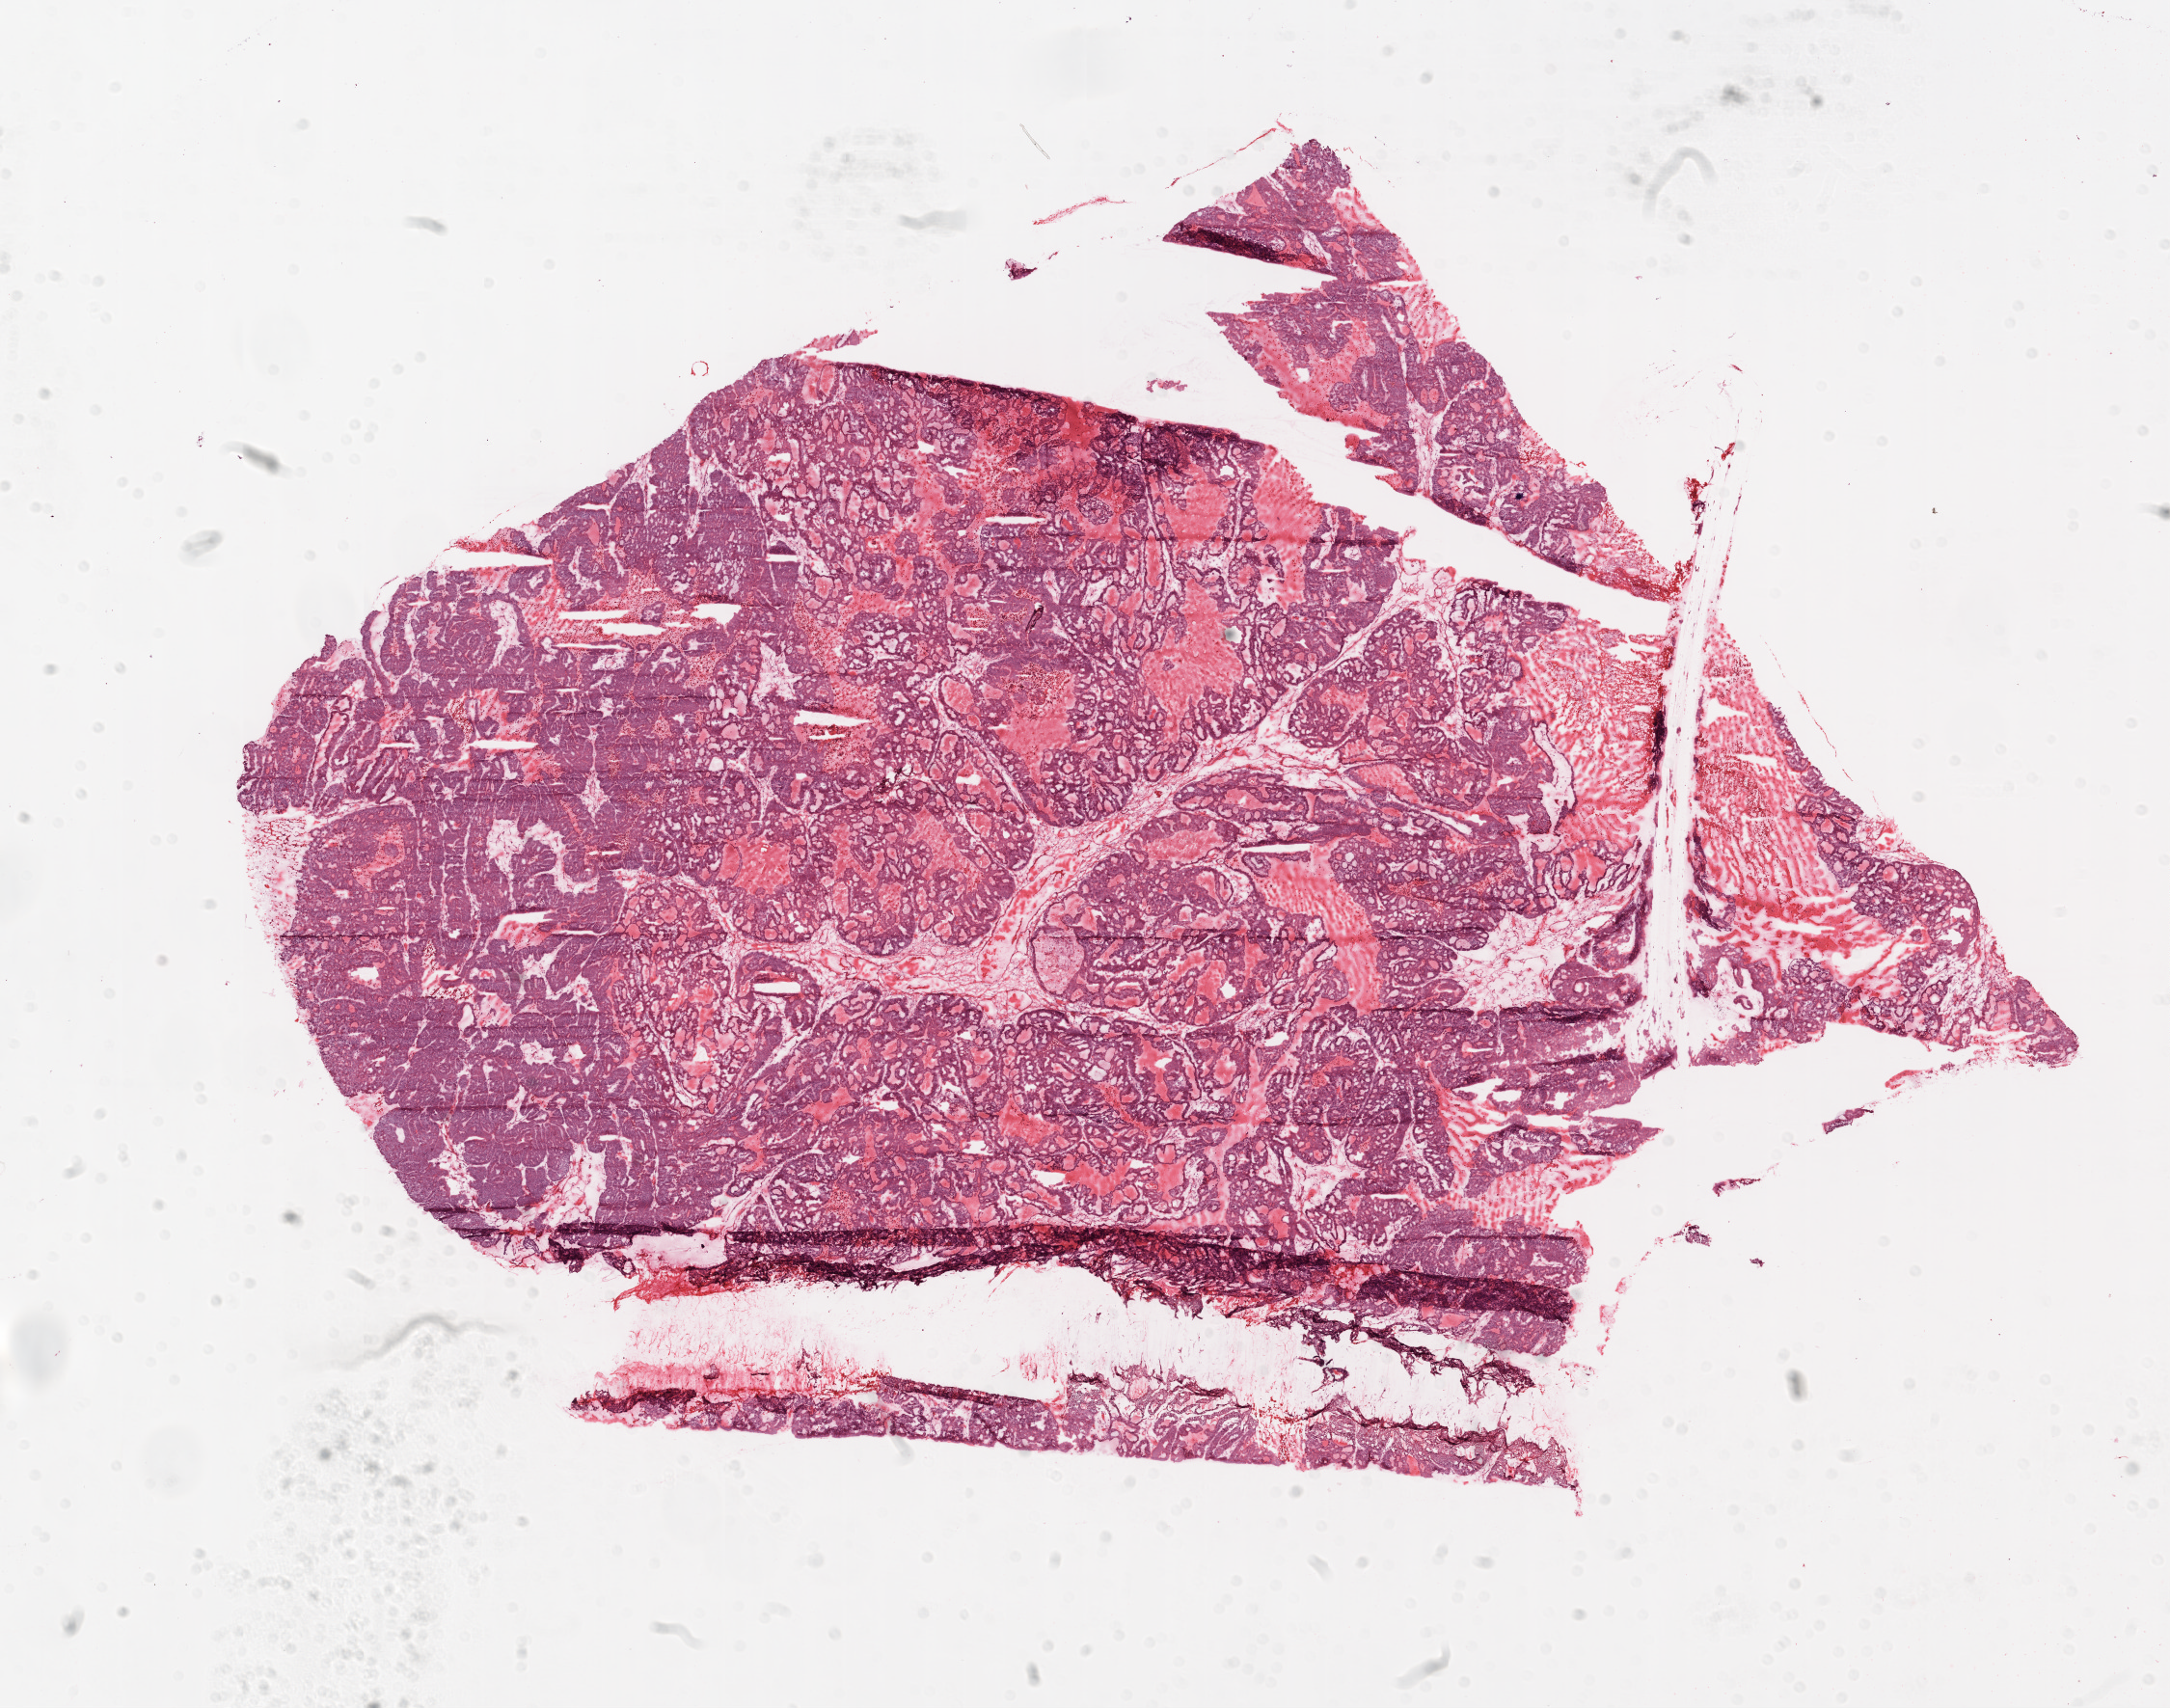
Digitized H&E tissue section (whole slide) — shown as a low-resolution overview of the whole scanned area (about 18.1 x 14.2 mm); frozen section from the top of the tissue portion; primary tumour sample from the ovary. Female, age 57 years at initial diagnosis. Pathologist review of this section (percent, as recorded): tumour cells 90%, tumour nuclei 99%.
Diagnosis: Serous cystadenocarcinoma, NOS.